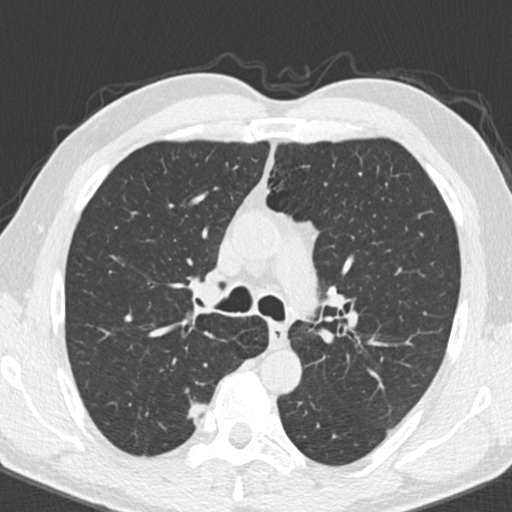
Low-dose screening chest CT, axial slice, third annual screen, lung window (W 1500 / L -600 HU), 2 mm slice thickness, 512 × 512 image matrix. Male participant, aged 55 years at enrolment. Current smoker at enrolment.
• Expert reader's lesion annotation, bounding box <171,396,217,438> (left, top, right, bottom; pixels).
• Reader record for this screening exam (exam-level; its link to the box is not recorded): non-calcified nodule or mass ≥4 mm, right upper lobe, 9 × 7 mm, smooth margins, soft tissue attenuation, pre-existing on the prior screen: no.
• Official screen result: positive, other.
• Lung cancer was diagnosed 221 days after this screen: adenocarcinoma, NOS, right upper lobe, poorly differentiated (G3), stage IA (AJCC 6th edition), 15 mm at pathology.